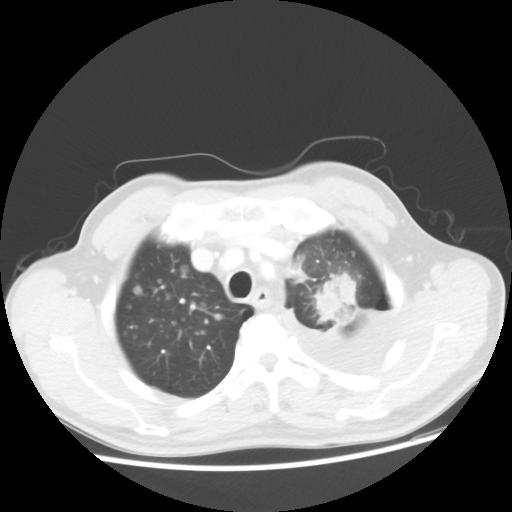
Chest CT, one axial slice; slice 40 of 48 in the series (ordered by position); reconstruction kernel STANDARD; 100 kVp; lung window (W 1500 / L -600 HU); 512 × 512 image matrix, field of view 362 × 362 mm. Male patient, age 55 years. From the clinical record (not read from this slice): clinical TNM (as recorded): T2 N3 M1a; histopathological grade: G3.
Outlined on this slice (rectangle marked by the reading radiologist):
- lung tumour (recorded histology: squamous cell carcinoma): bounding box [x1, y1, x2, y2] px = [318, 272, 363, 328]